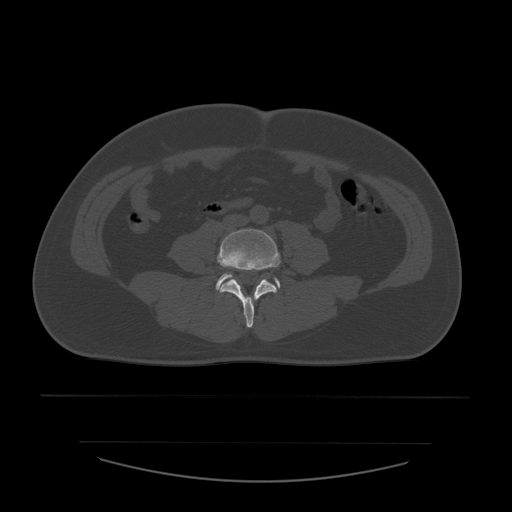
CT including the spine, one axial slice; position 139 of 532 along the scan axis; bone window (W 1800 / L 400 HU); 1.25 mm slice thickness; 512 × 512 image matrix, field of view 441 × 441 mm. Patient age 44 years. Case-level facts recorded for this patient, not image findings: primary cancer: soft tissue sarcoma.
Structures marked on this image (semi-automatically segmented with operator editing):
- L4 vertebra: box from (x=217, y=229) to (x=280, y=328) px
- L5 vertebra: (x=216, y=274)–(x=281, y=290)